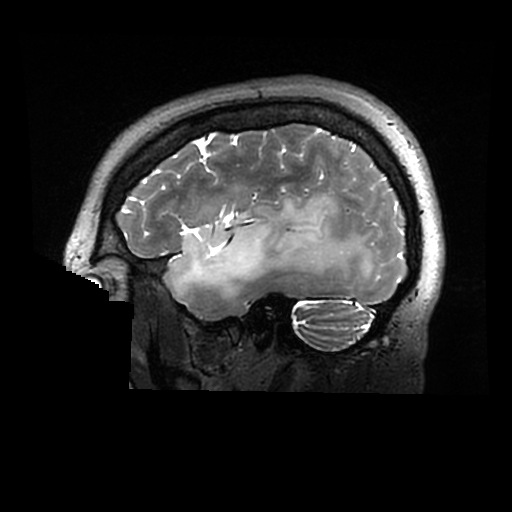
Brain MRI from a brain-tumour surgery series, one sagittal slice; position 227 of 320 along the scan axis; 0.6 mm slice thickness; 512 × 512 image matrix, field of view 240 × 240 mm. From the clinical record (not read from this slice): histopathology: Astrocytoma; WHO grade: 2; IDH mutation: yes.
Annotated regions visible in this slice (expert manual segmentation):
- tumour: bounding box <167,194,378,298> (left, top, right, bottom; pixels)